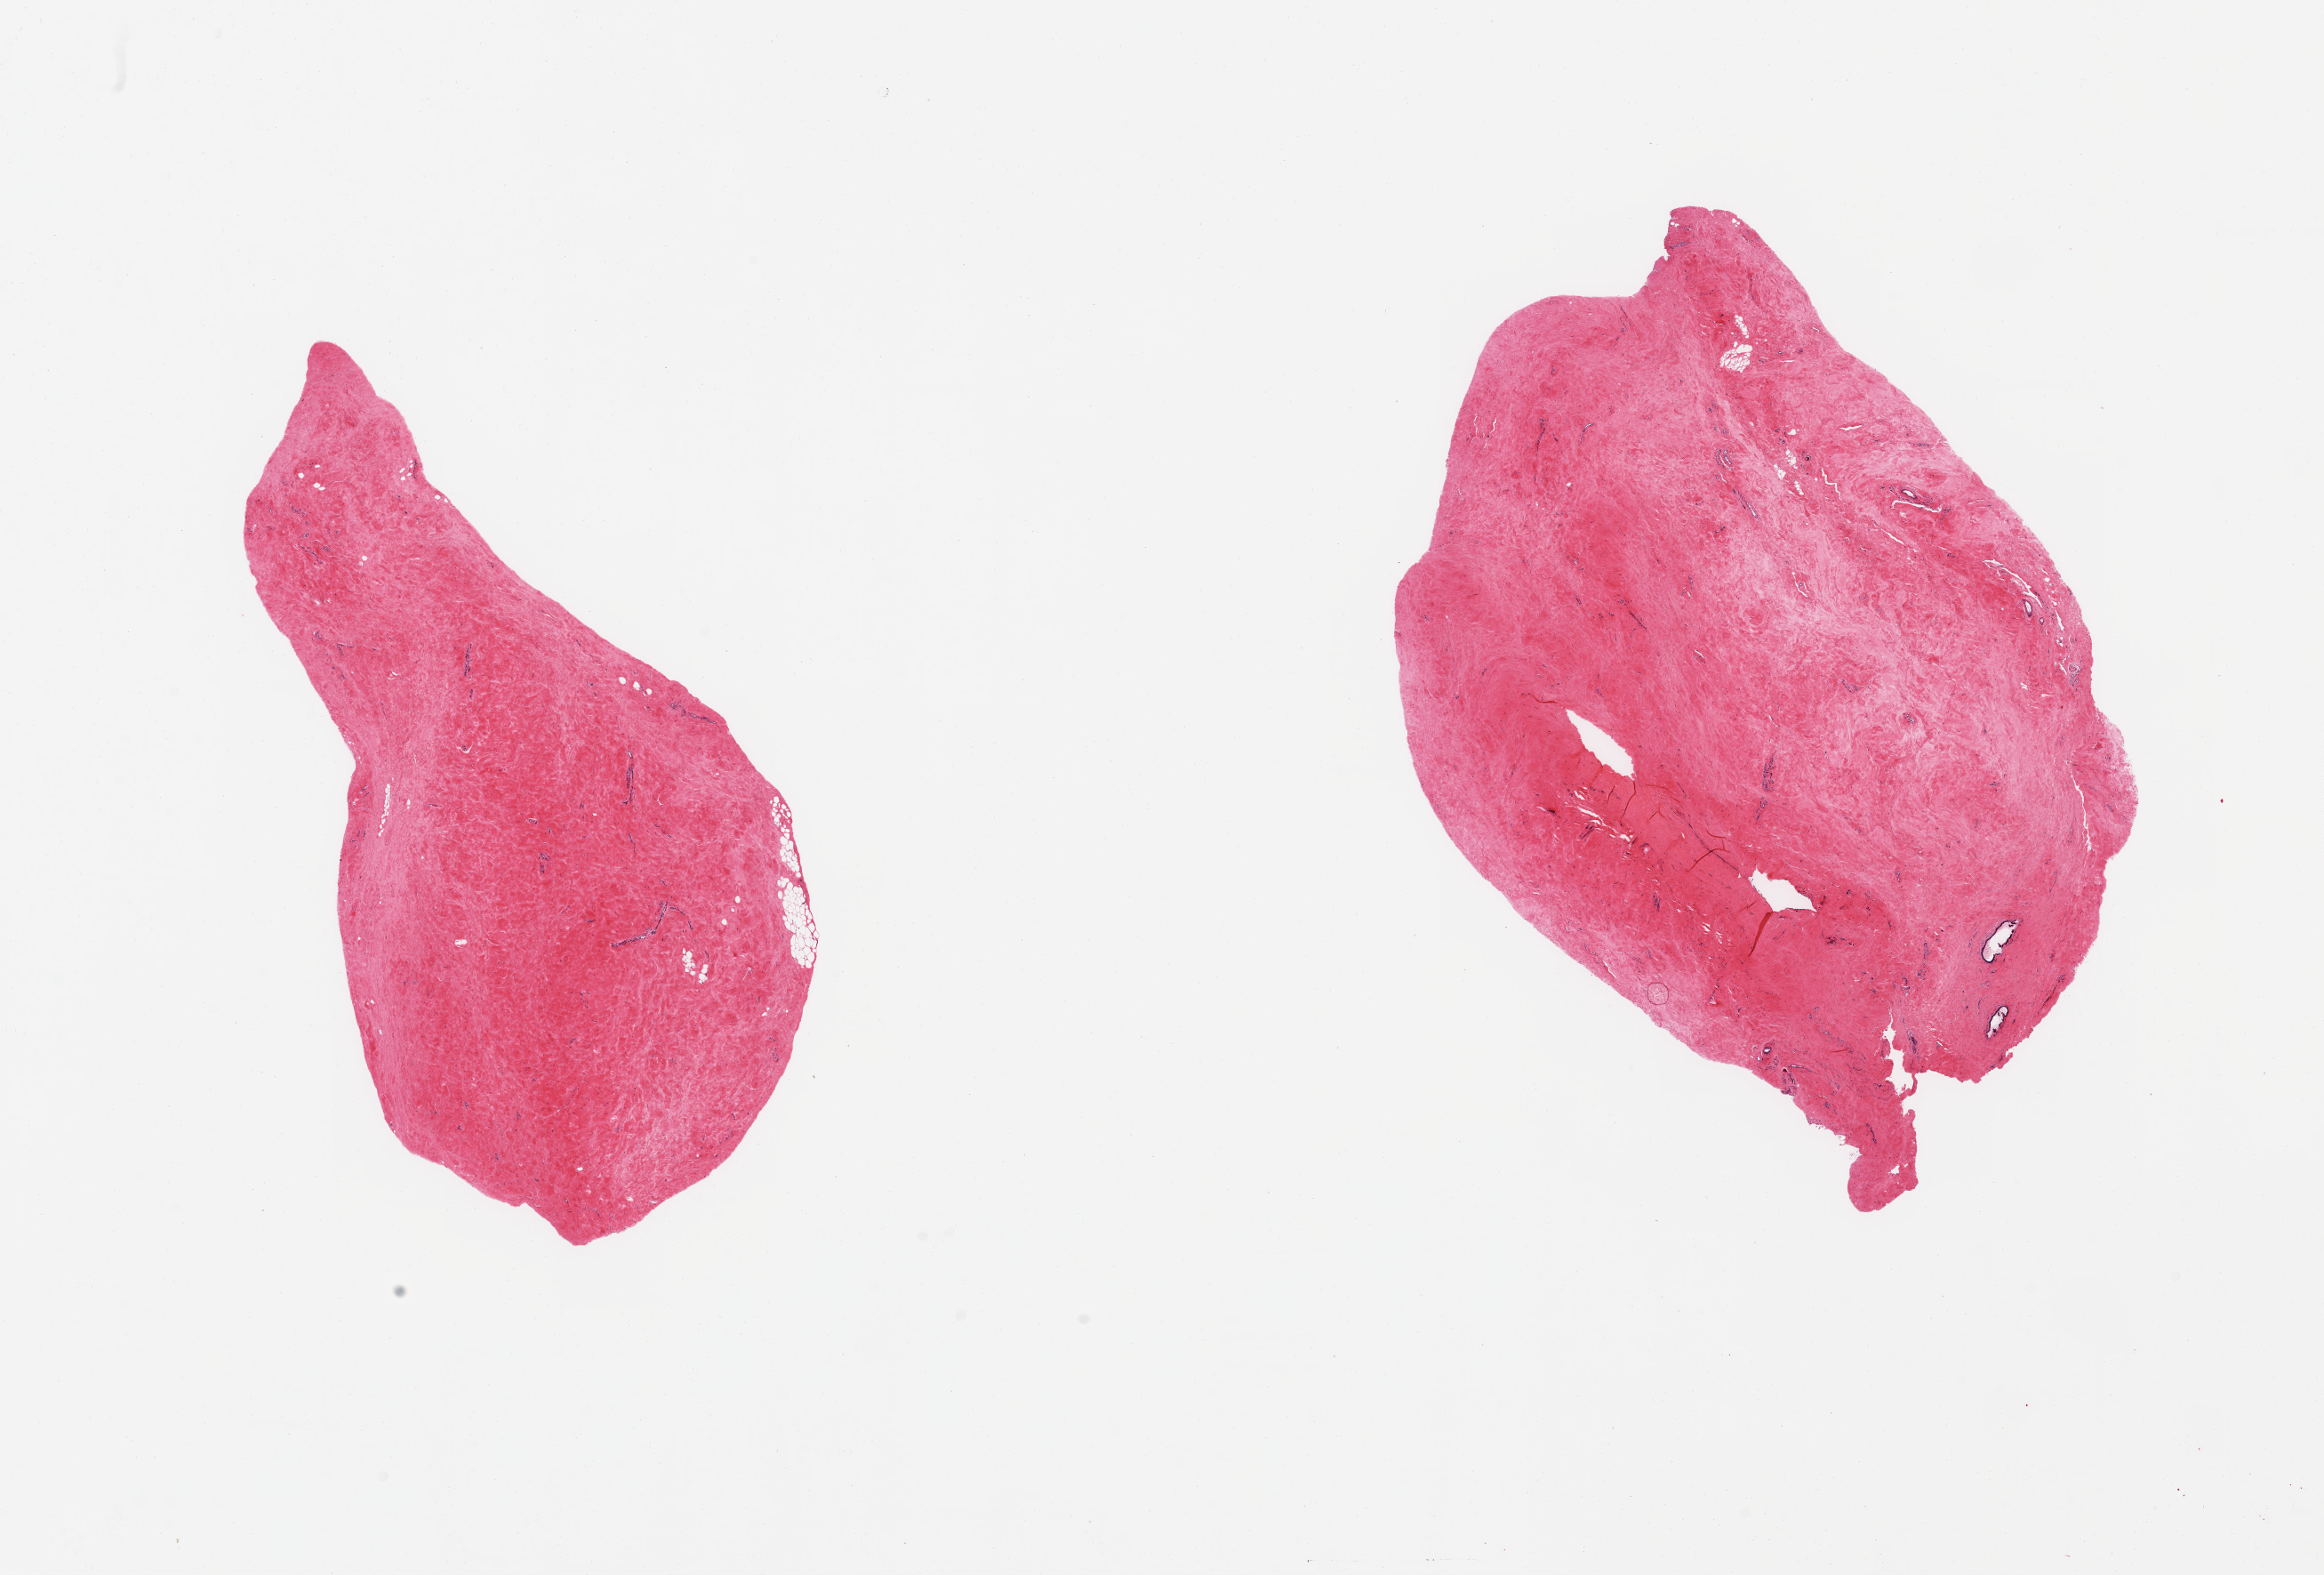
Whole-slide image, H&E stain, a low-resolution overview of the entire scanned area, about 20.7 x 14.0 mm, PAXgene-fixed, paraffin-embedded tissue, section of breast (target tissue), donor tissue sample.
Reviewer comment on this tissue sample: 2 pieces; densely fibrotic stroma with few mammary ducts.